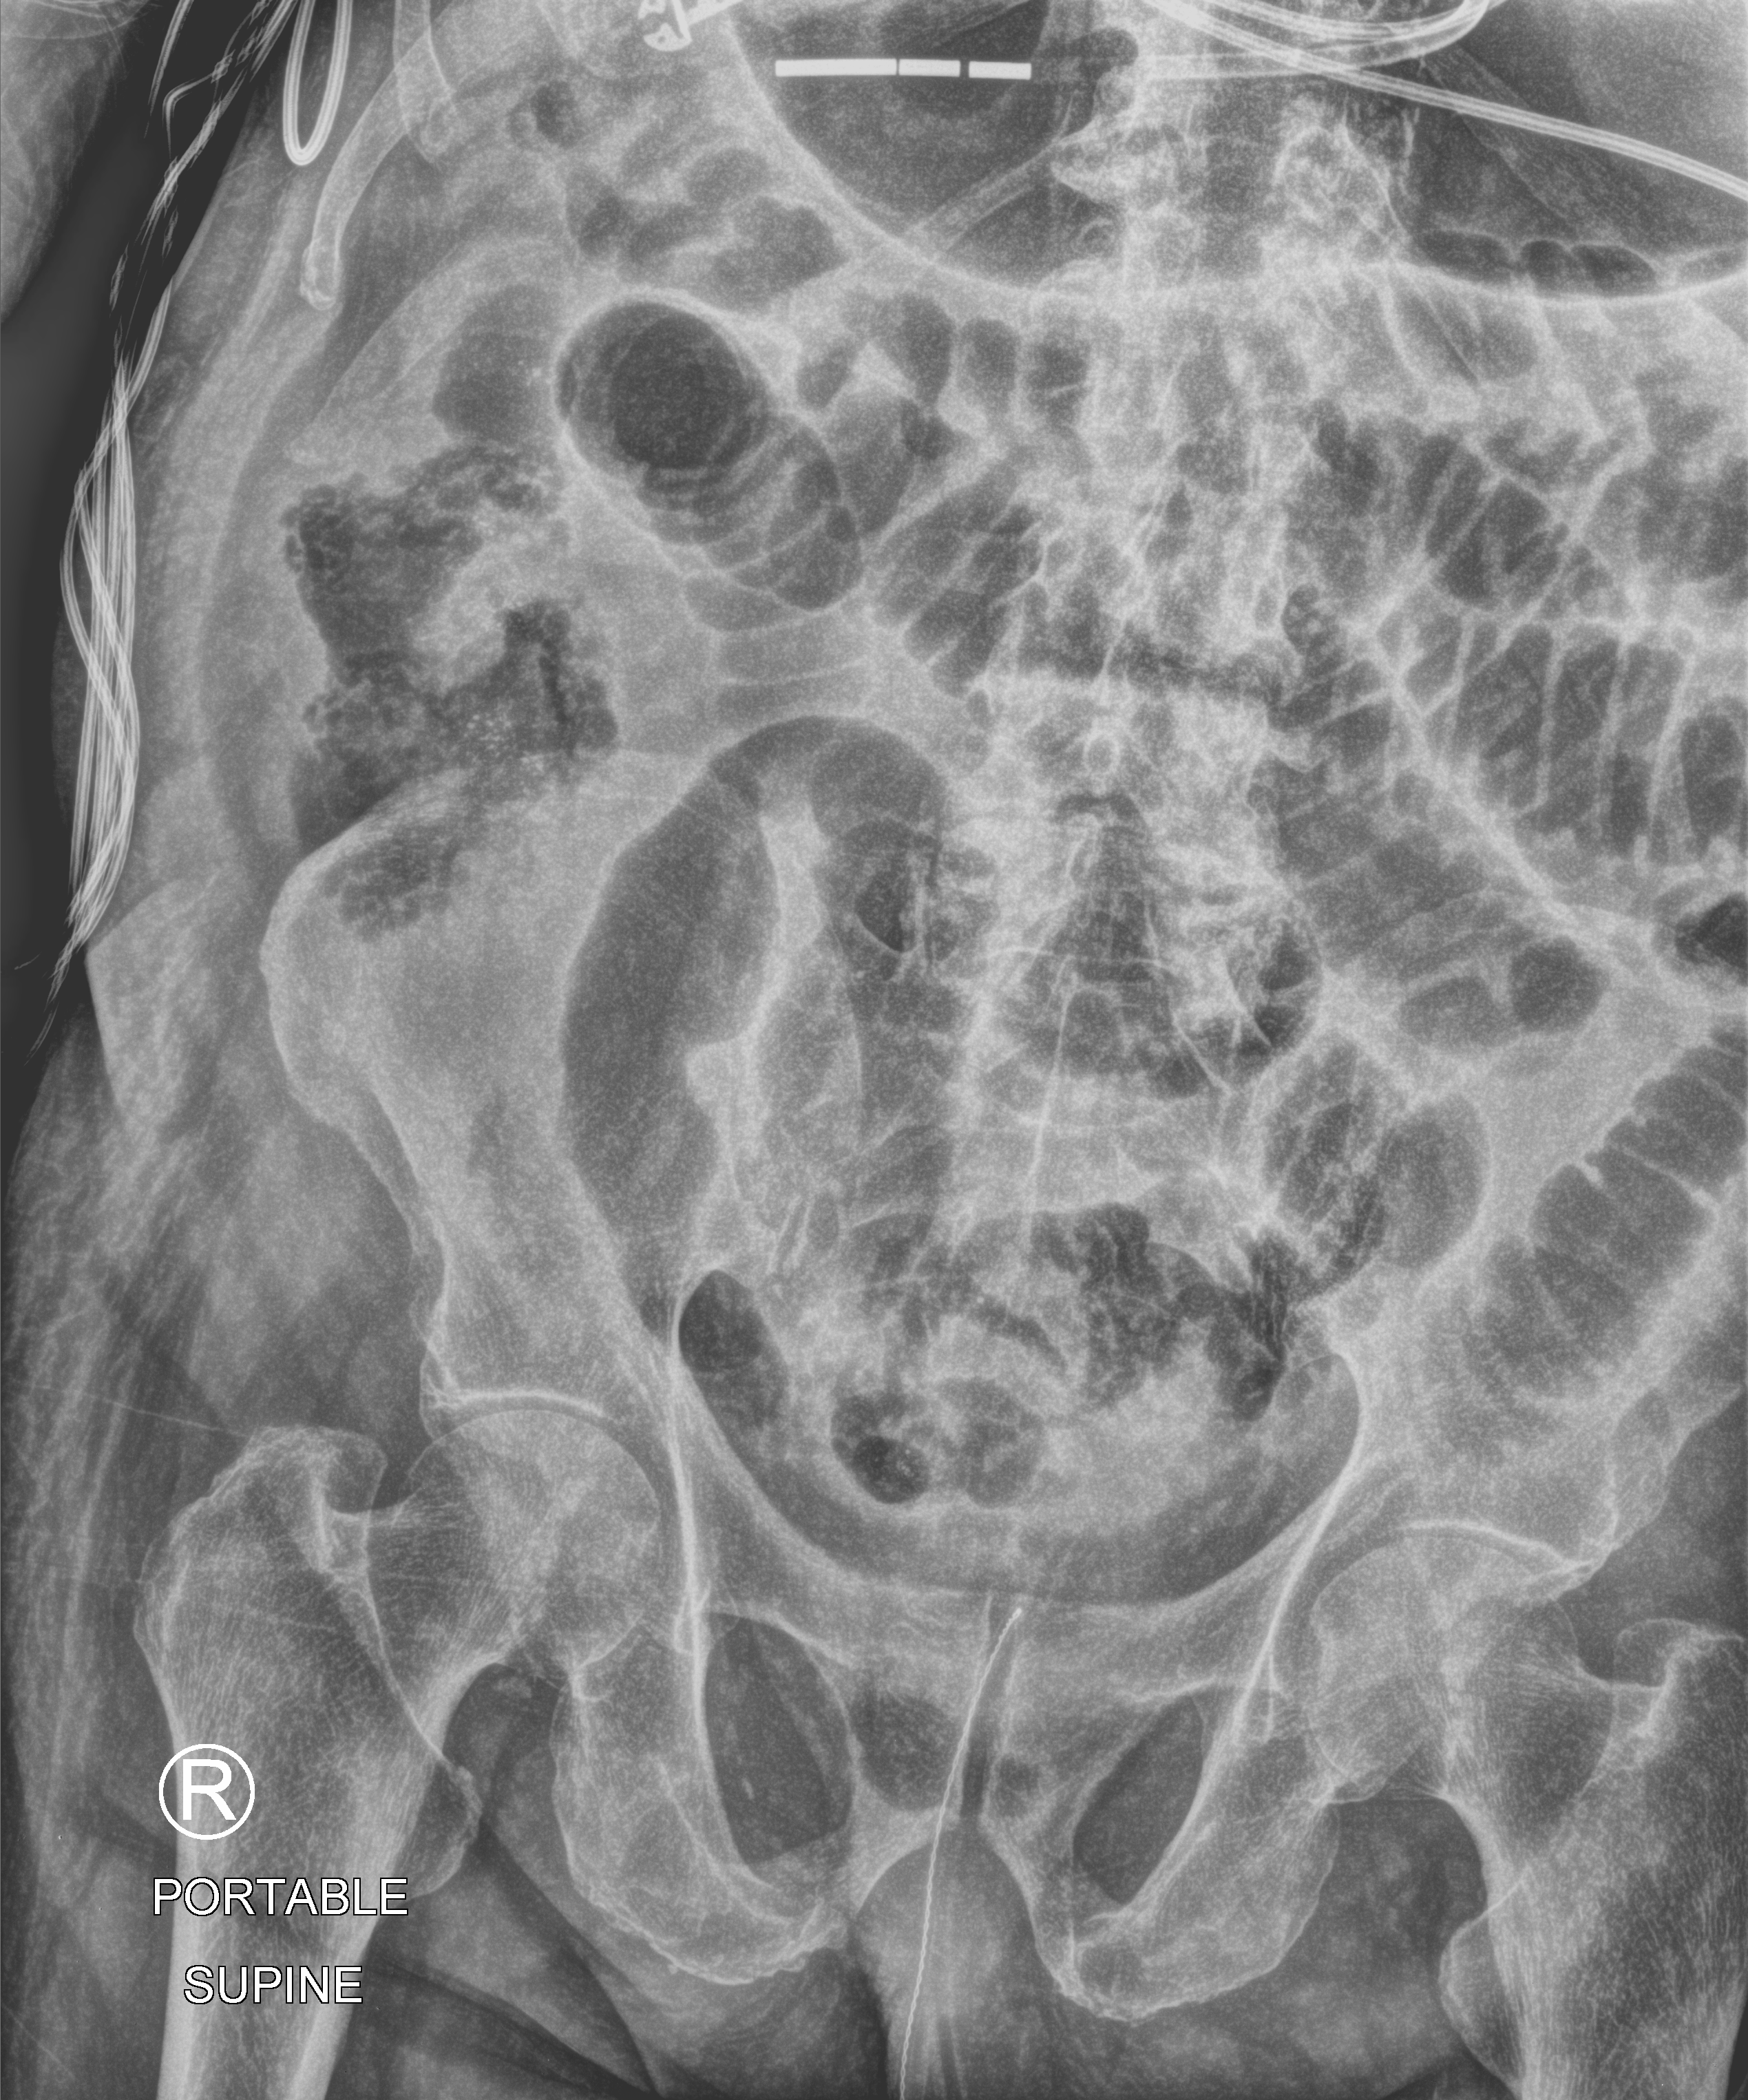
Bedside abdomen radiograph (computed radiography); anteroposterior (AP) projection. Male patient hospitalised with COVID-19, age 75–90 years.
From the hospital-stay record, not from the radiograph (when in the stay this image was taken is not recorded): admitted to intensive care during this hospital stay: yes; mechanically ventilated during this hospital stay: yes.